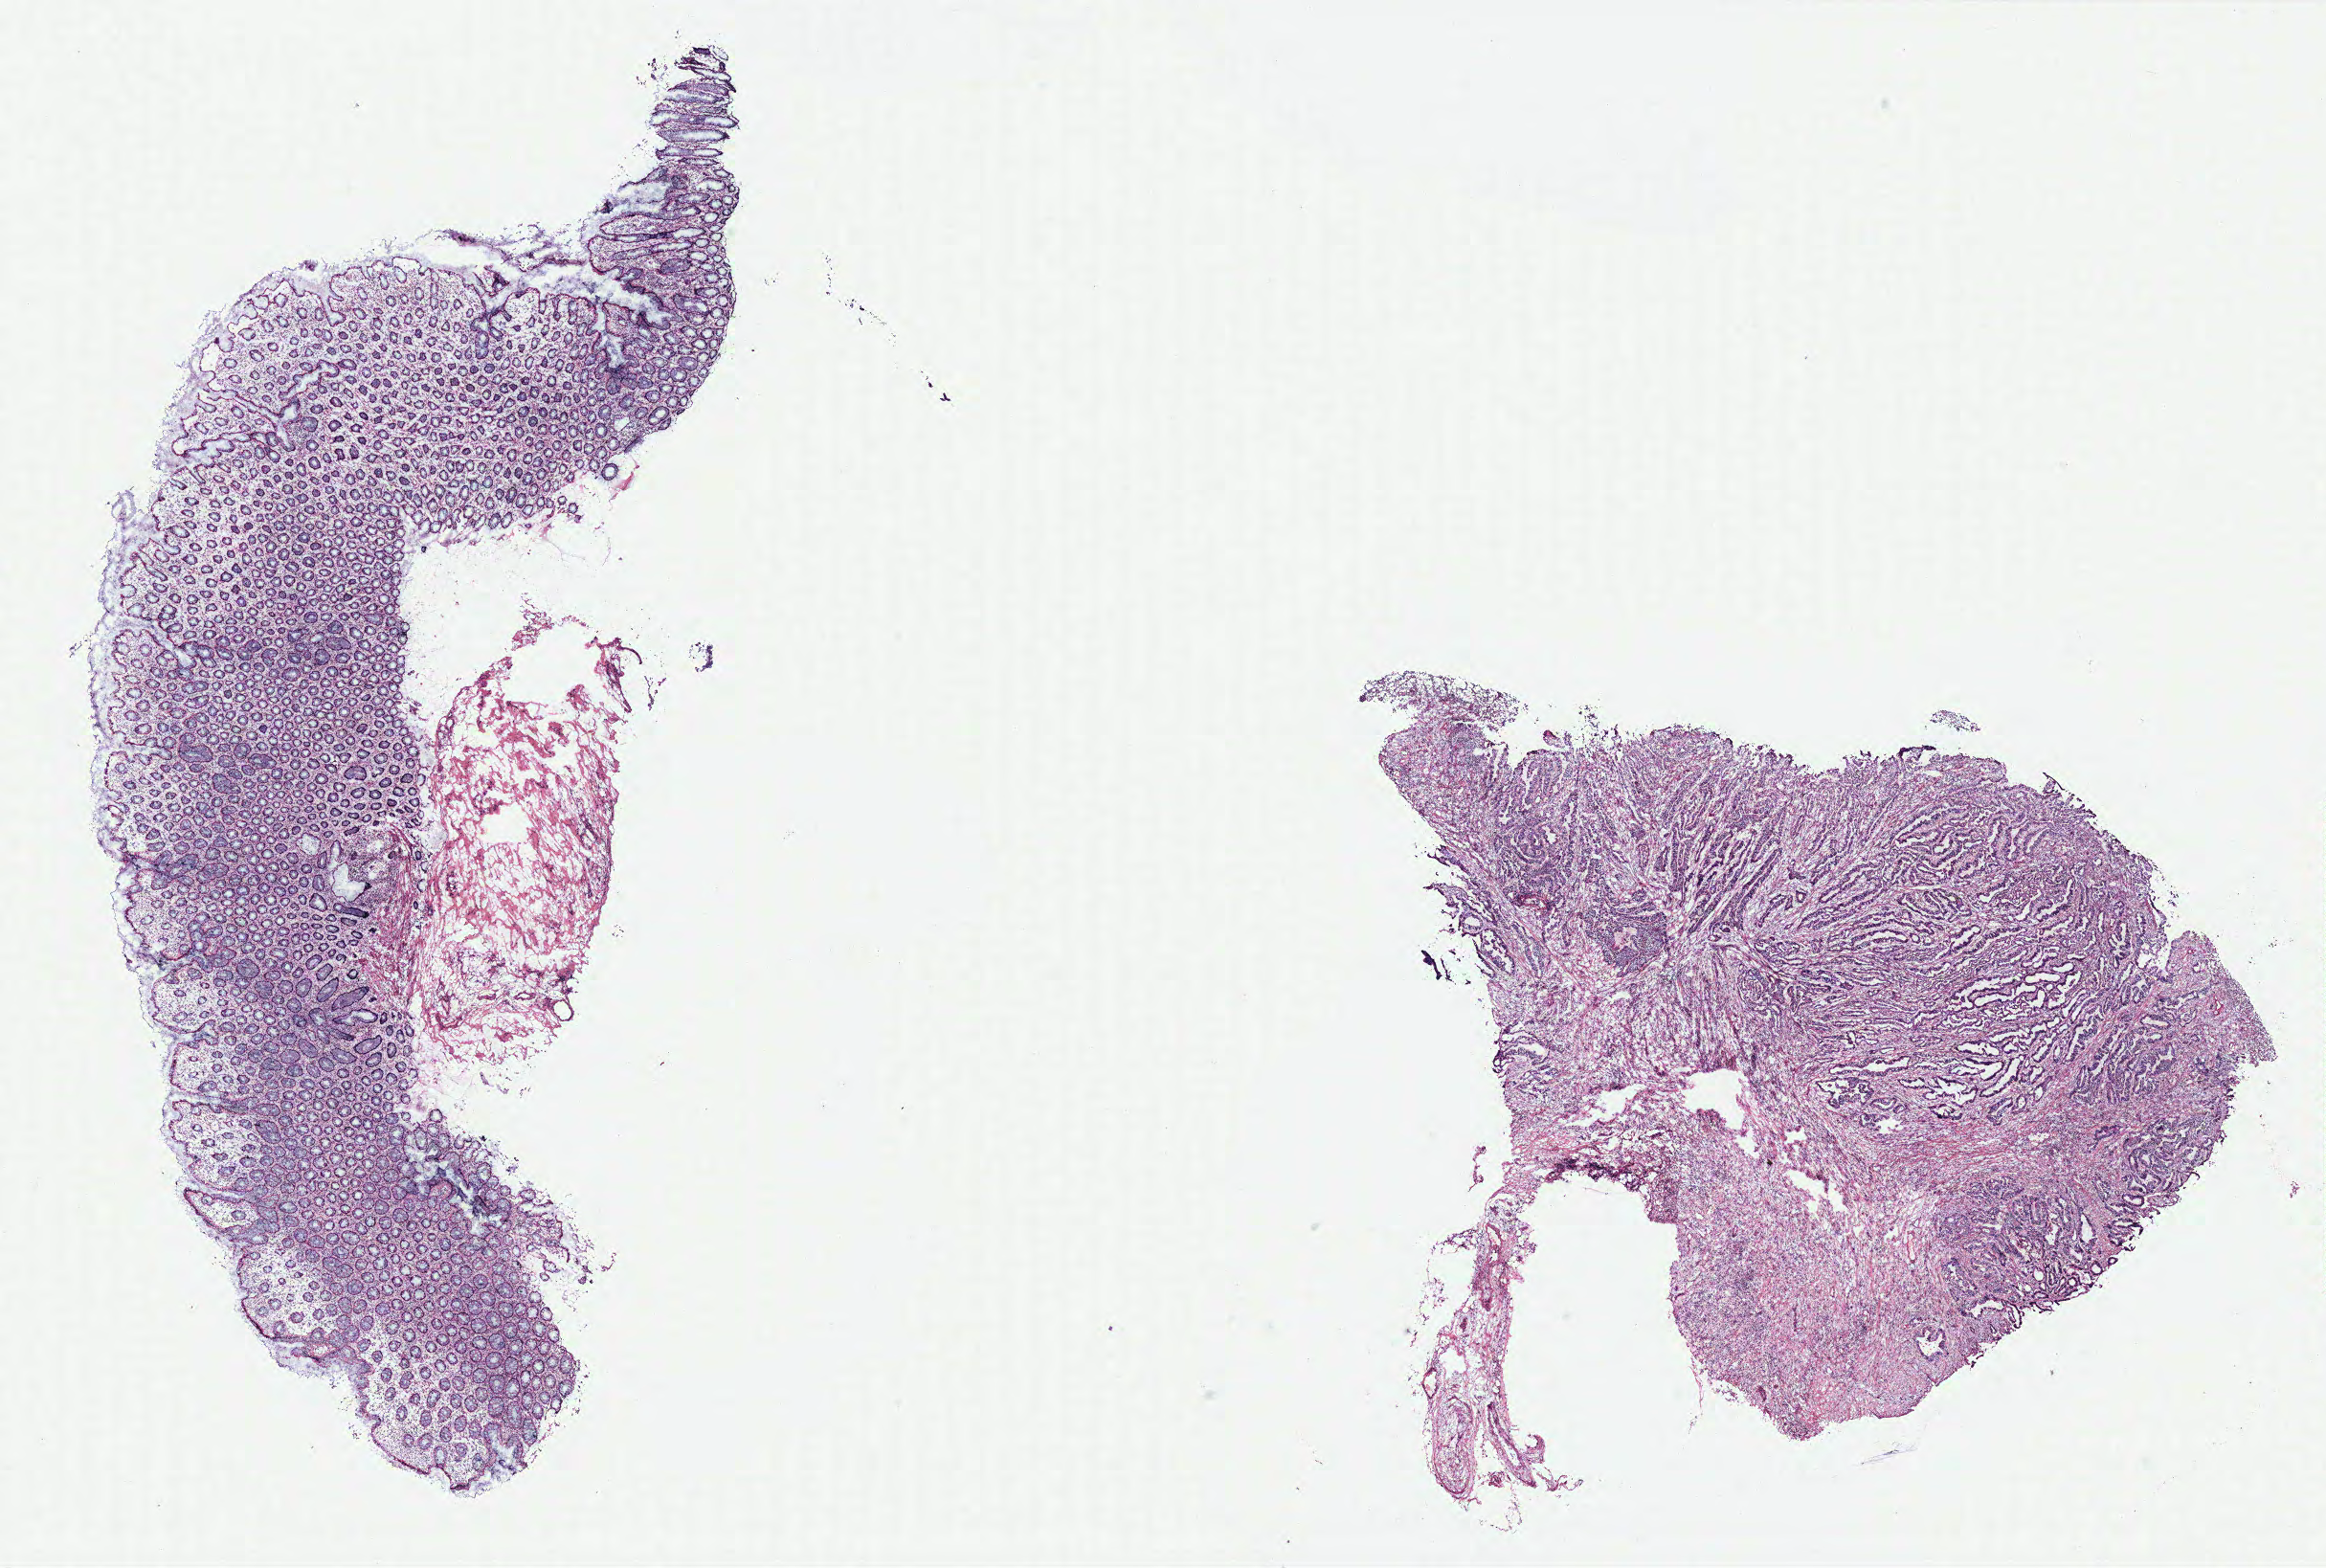
Digitized H&E tissue section (whole slide), whole scanned area (about 19.4 x 13.1 mm, acquisition: 40x scan) shown as a low-resolution overview, colon, tissue type not recorded.
Patient diagnosis (cohort enrolment): colon cancer (colon).